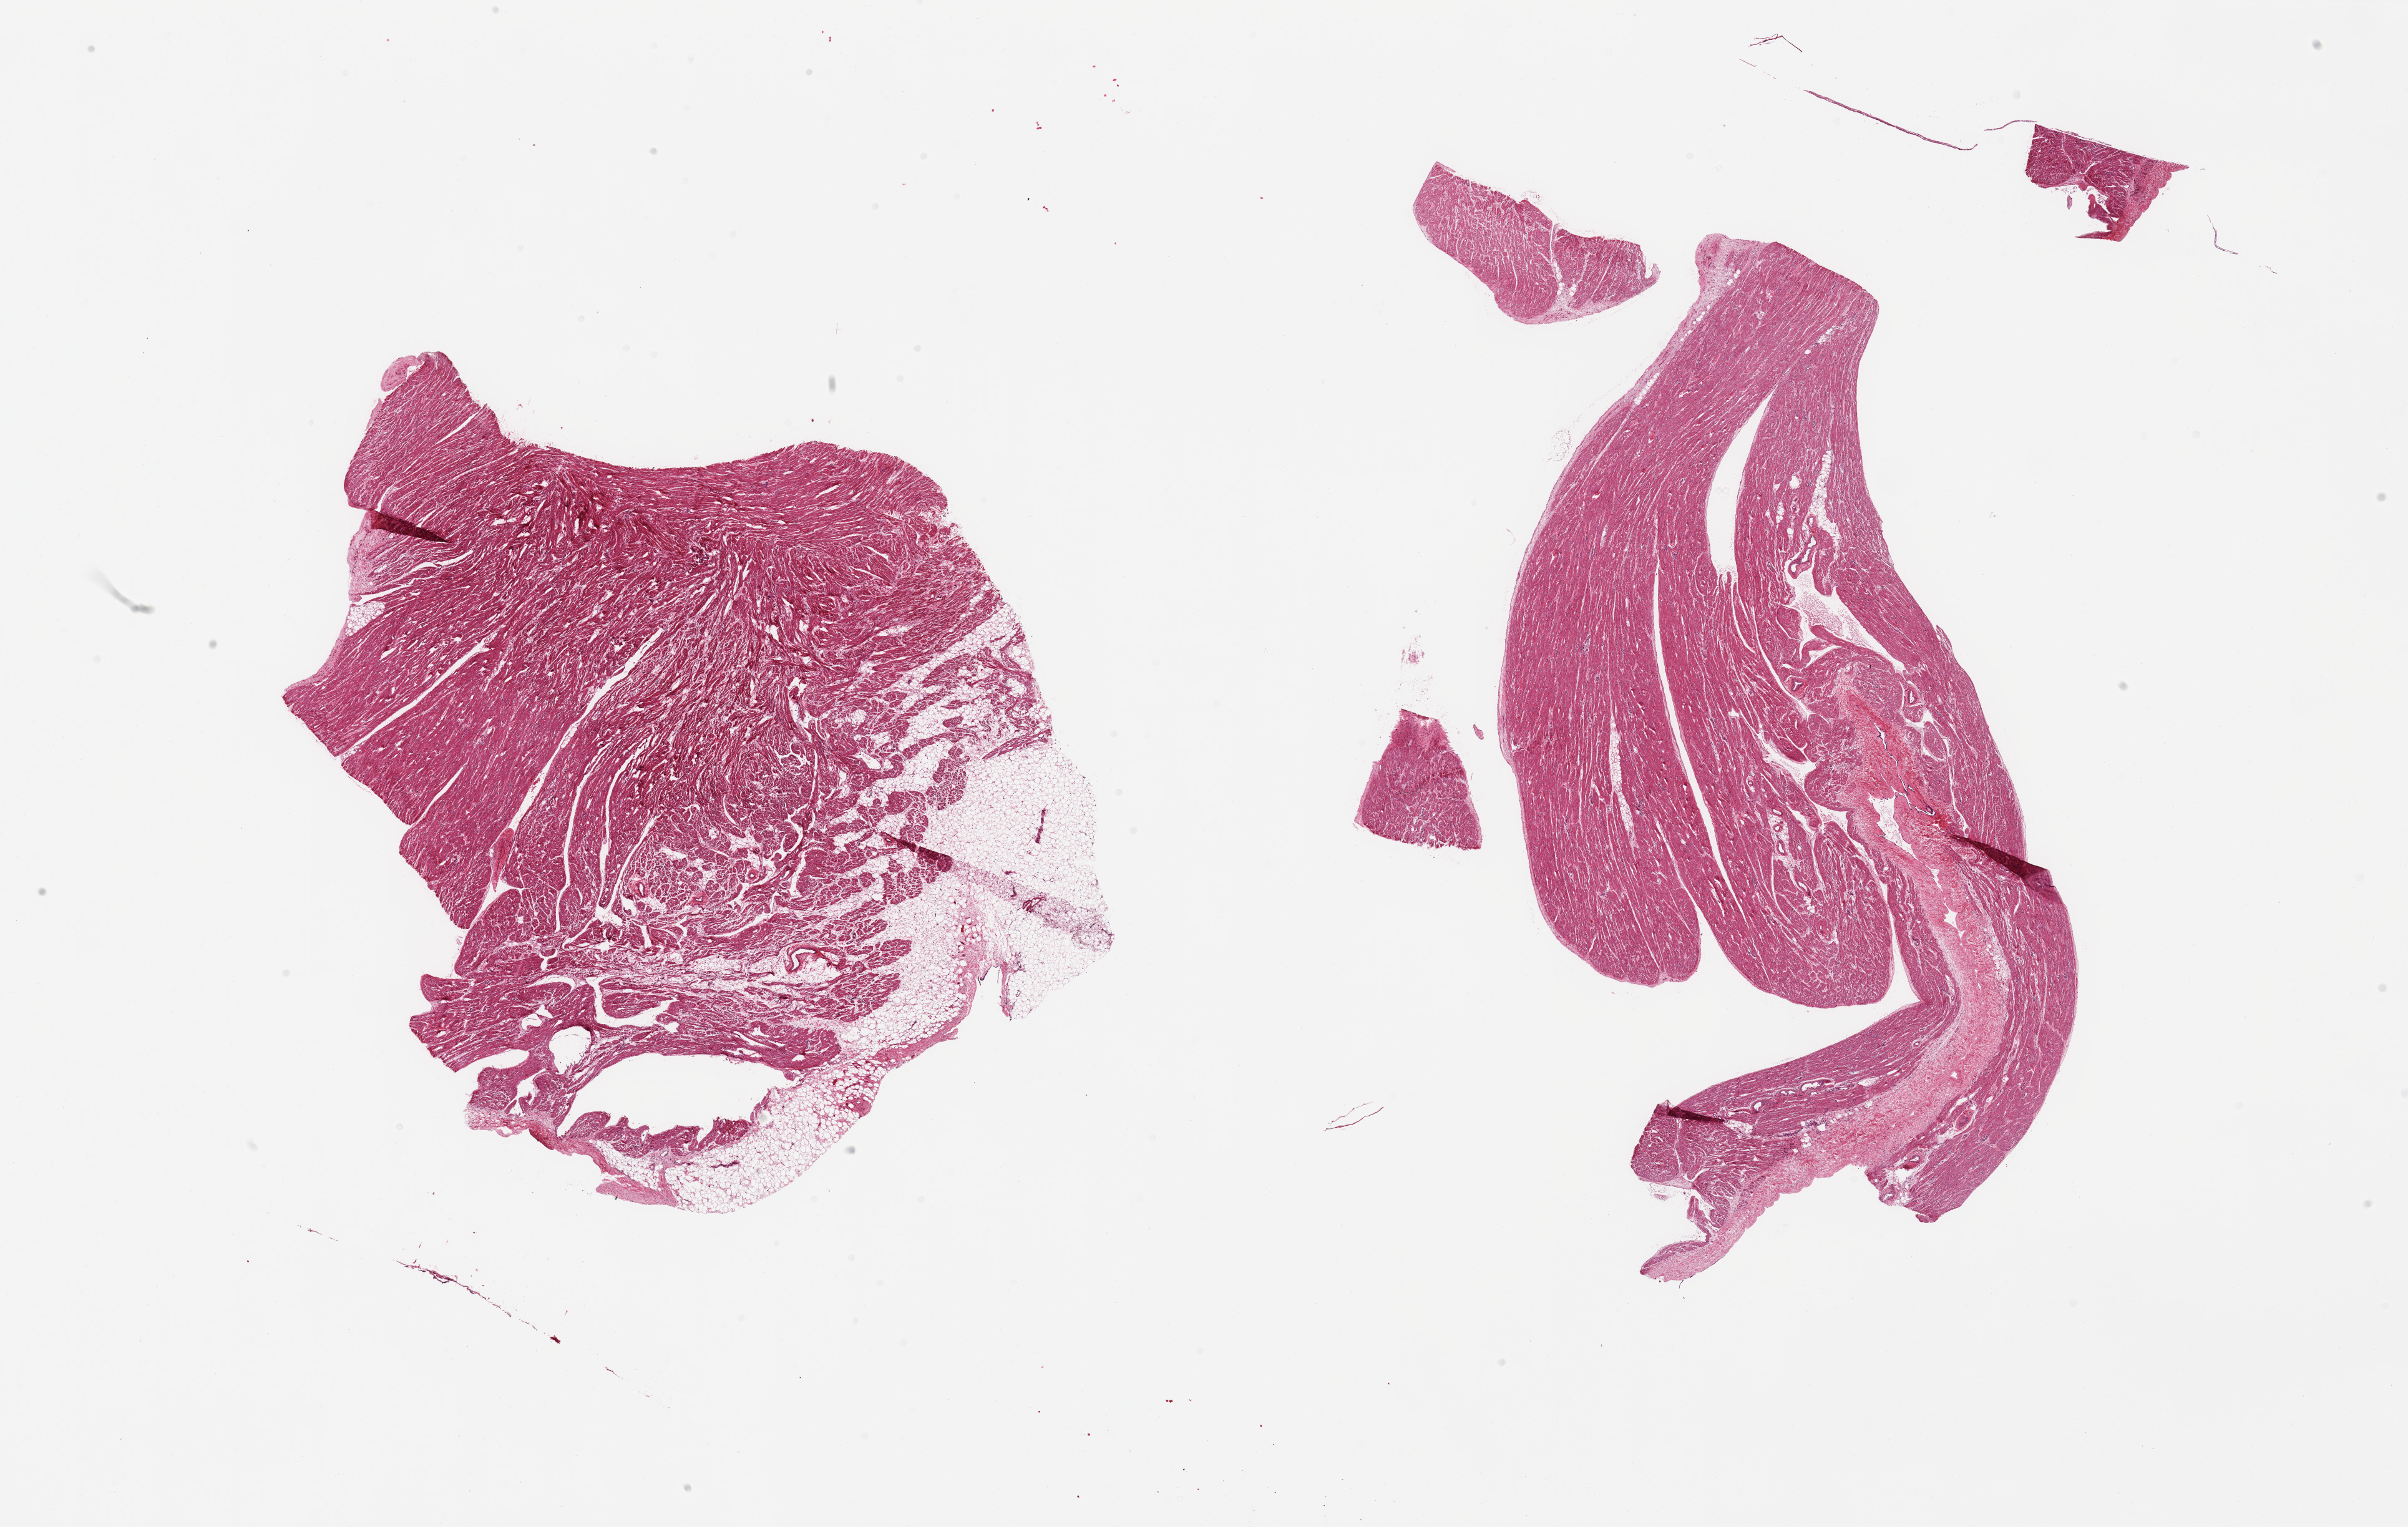
Digitized H&E-stained section — a low-resolution overview of the entire scanned area, about 30.5 x 19.4 mm, PAXgene-fixed paraffin-embedded (PFPE) section, target tissue: auricular appendage, tissue donor sample. Female donor.
Reviewer comment on this tissue sample: 2 pieces; one piece is ~15% fat.